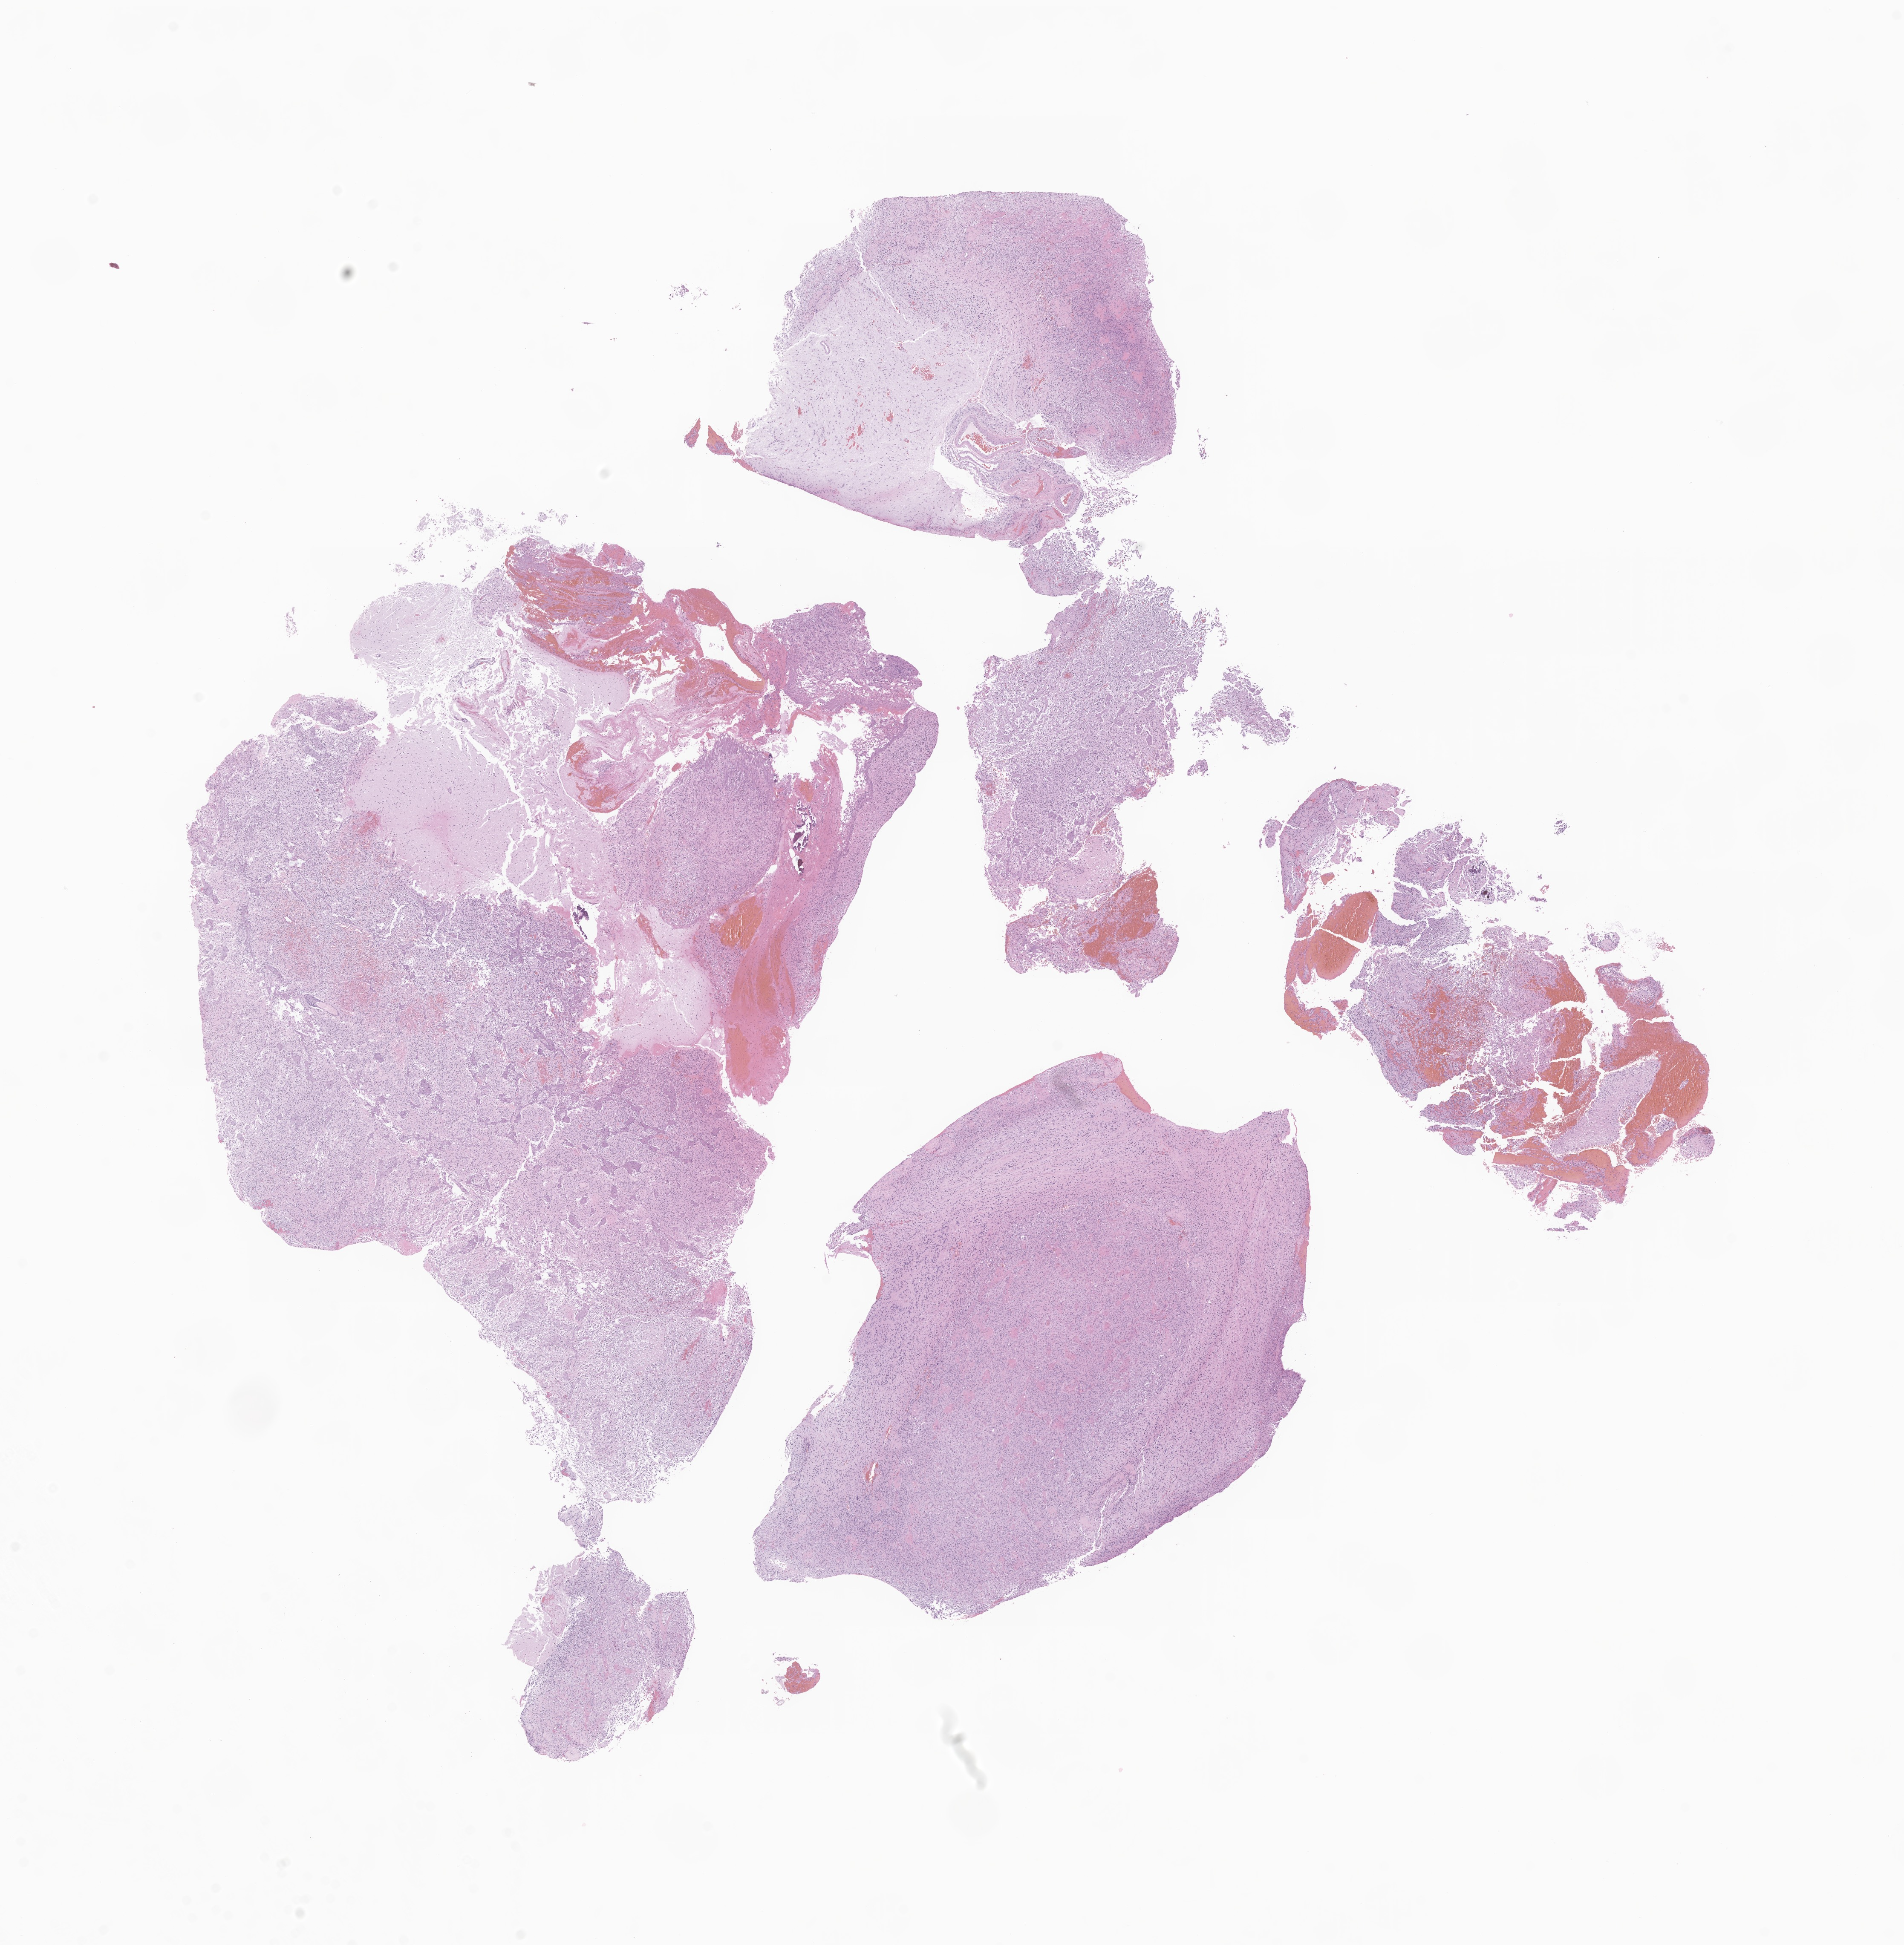
Digitized H&E-stained section of tumor tissue from the brain — shown as a low-resolution overview of the whole scanned area (about 18.8 x 19.2 mm). Formalin-fixed, paraffin-embedded (FFPE) tissue. Male patient, age 45 months (3 years 9 months).
- recorded diagnosis: Ependymoma, NOS